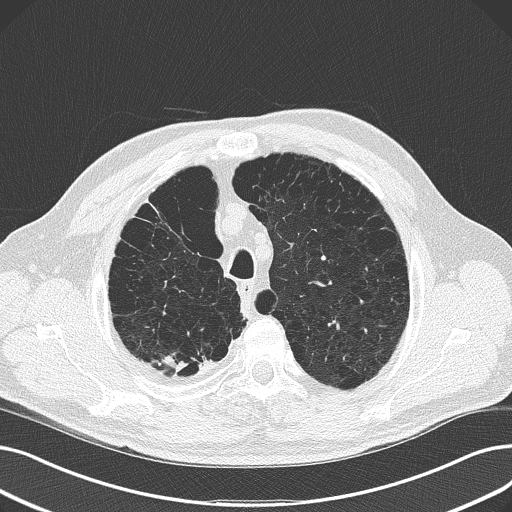
Low-dose screening chest CT, axial slice; second screening round (one year after baseline); lung window (W 1500 / L -600 HU); 2 mm slice thickness; lung (sharp) reconstruction kernel (B50f). Male, age 68 years at enrolment. Current smoker at enrolment.
Lesion marked by an expert reader, bounding box [x1, y1, x2, y2] px = [143, 333, 223, 390]. The screening reader recorded 4 non-calcified nodules or masses ≥4 mm on this exam (right upper lobe, left lower lobe, left upper lobe, right lower lobe); which of them this box marks is not recorded. Later outcome: lung cancer diagnosed 304 days after this screen — adenocarcinoma, NOS, right upper lobe, stage IV (AJCC 6th edition), 29 mm at pathology.